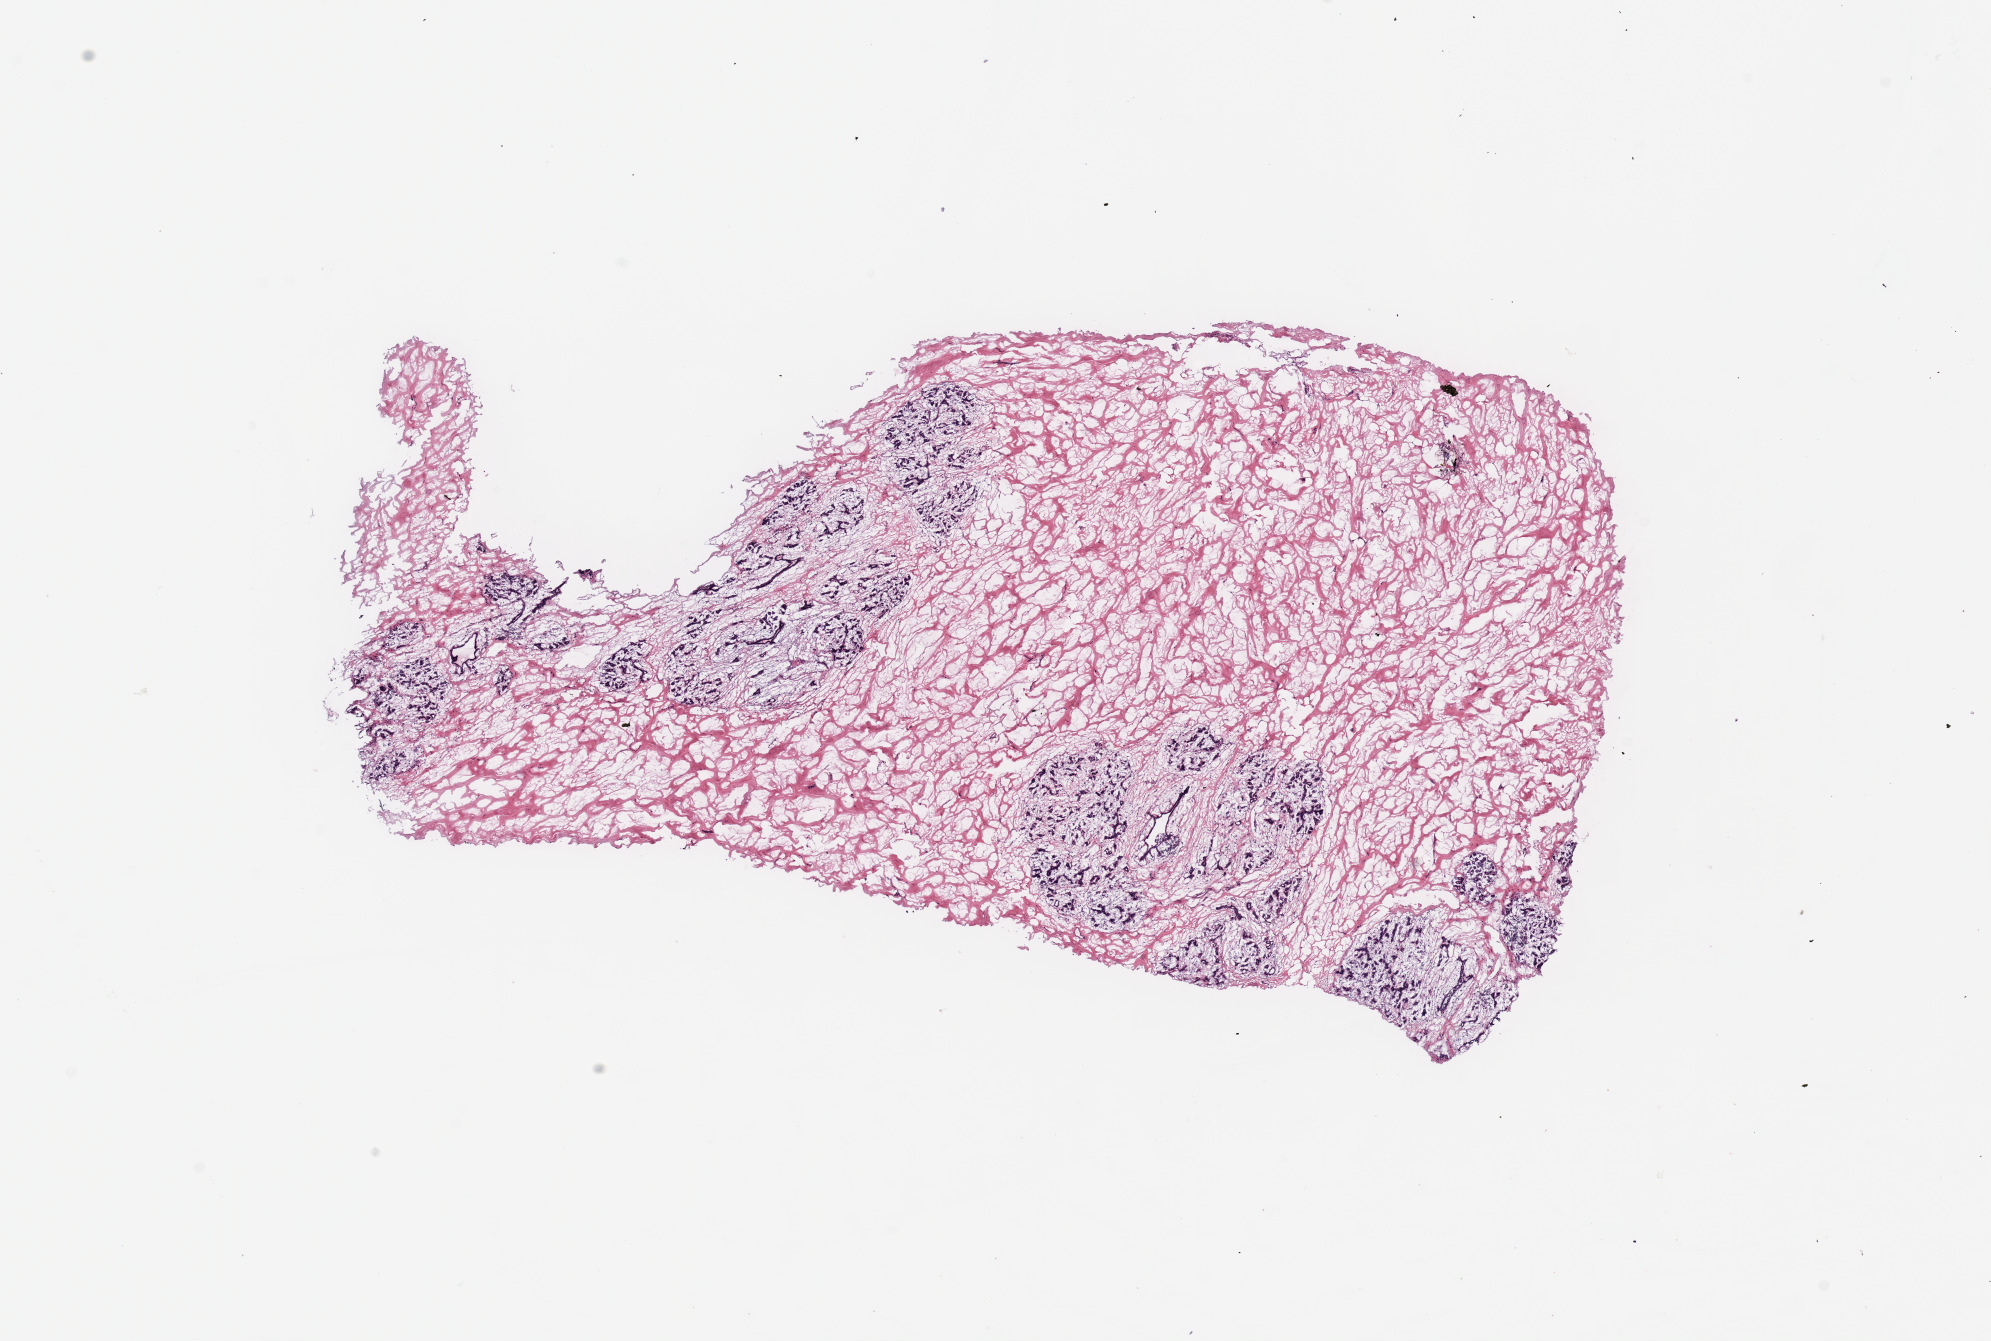
H&E whole-slide image, a low-resolution overview of the entire scanned area, about 15.8 x 10.6 mm (acquisition: 20x scan); breast, tissue type not recorded.
Patient diagnosis (cohort enrolment): breast cancer (breast).